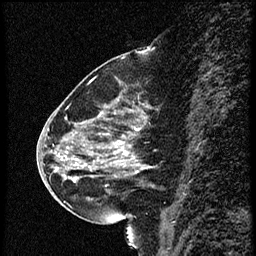
Breast MRI (dynamic contrast-enhanced), one sagittal slice; slice 25 of 56 in the series (ordered by position); dynamic contrast-enhanced study with each time point stored as its own series, time point 2 of 4 at this slice position (early post-contrast, ordered by acquisition time); 1.5 T; TE 4.2 ms, TR 18.9 ms; 2 mm slice thickness; 256 × 256 image matrix, field of view 200 × 200 mm. Female patient. Case-level facts recorded for this patient, not image findings: setting: breast cancer imaged before/during neoadjuvant chemotherapy; receptor status: HER2-positive.
Structures marked on this image (semi-automatically segmented with operator editing):
- analysis volume of interest (the breast-tissue region the enhancement analysis was run in; not a lesion): bounding box <63,80,169,215> (left, top, right, bottom; pixels)
- tumour enhancement mask (voxels above the 100 % enhancement threshold inside the analysis volume of interest): <67,140,139,183>